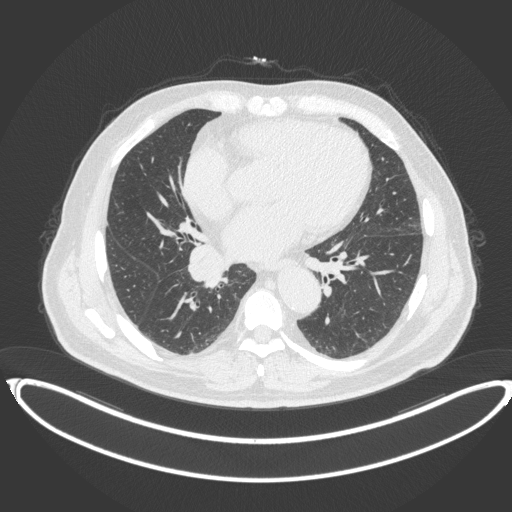
Chest CT, one axial slice; position 185 of 383 along the scan axis; reconstruction kernel B31f; 120 kVp; lung window (W 1500 / L -600 HU); 1 mm slice thickness; 512 × 512 image matrix, field of view 448 × 448 mm. Male patient, age 61 years. Case-level facts recorded for this patient, not image findings: clinical TNM (as recorded): T1b N1 M0.
Outlined on this slice (rectangle marked by the reading radiologist):
- lung tumour (recorded histology: squamous cell carcinoma): bounding box (x1, y1, x2, y2) in pixels: (188, 243, 229, 290)